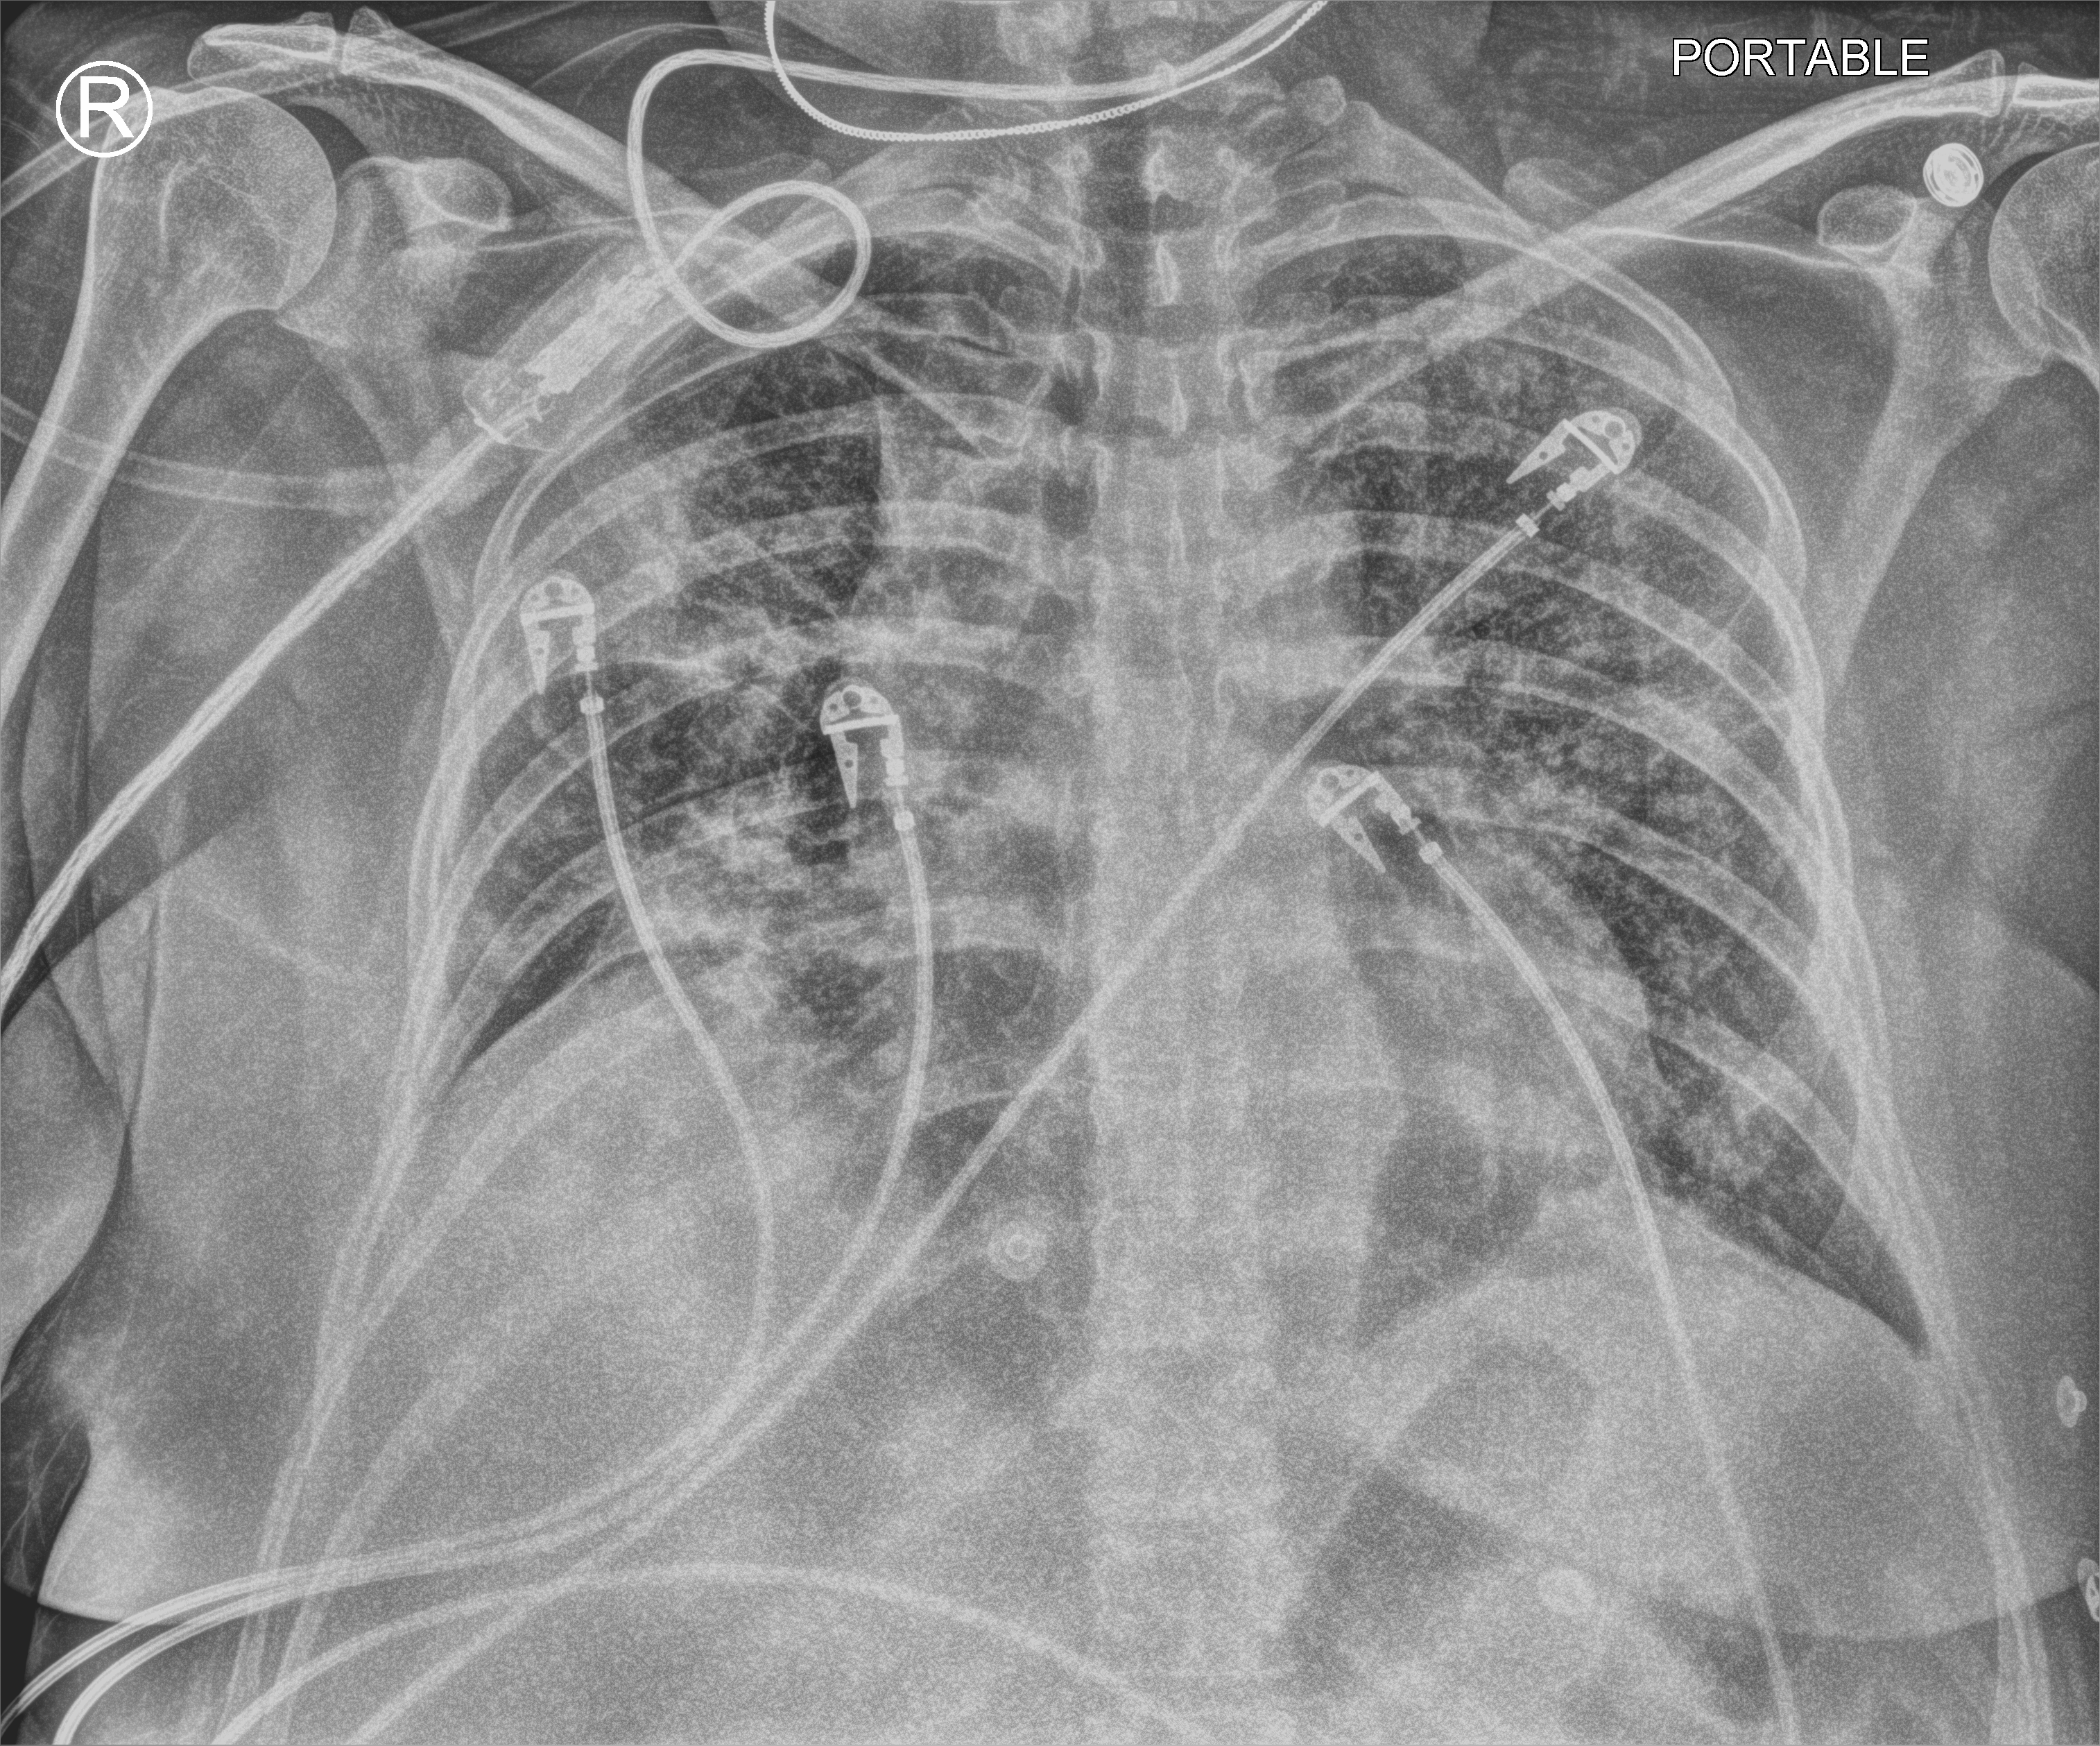
Bedside chest radiograph (computed radiography). Patient hospitalised with COVID-19; female, aged 18–59 years.
Admission-level facts for this patient (not findings on this image; timing relative to this image not recorded): admitted to intensive care during this hospital stay: yes; mechanically ventilated during this hospital stay: yes.